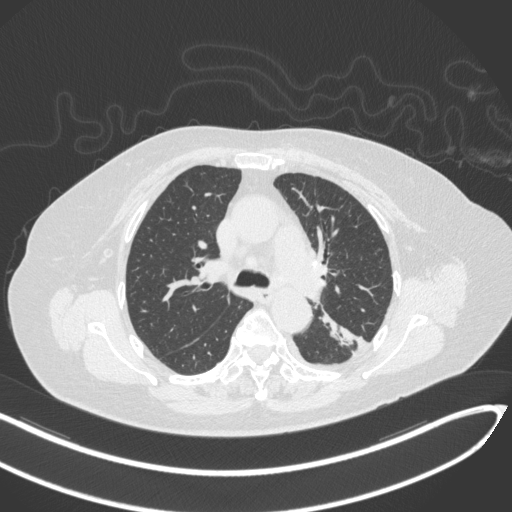
Chest CT, one axial slice; slice 207 of 270 in the series (ordered by position); reconstruction kernel B31f; 120 kVp; lung window (W 1500 / L -600 HU); 1 mm slice thickness; 512 × 512 image matrix, field of view 400 × 400 mm. Female patient, age 76 years. From the clinical record (not read from this slice): clinical TNM (as recorded): T1c N0 M0.
Annotated regions visible in this slice (rectangle marked by the reading radiologist):
- lung tumour (recorded histology: adenocarcinoma): bounding box (x1, y1, x2, y2) in pixels: (317, 310, 357, 347)